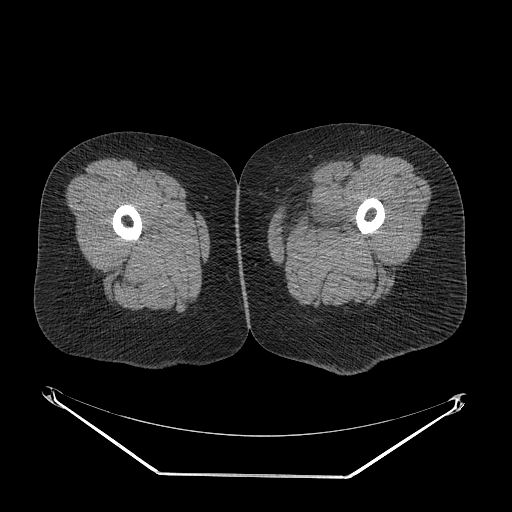
CT of an extremity soft-tissue mass (from a PET/CT study), one axial slice. Position 12 of 267 along the scan axis. Reconstruction kernel STANDARD. Soft-tissue window (W 400 / L 40 HU). 3.75 mm slice thickness. 512 × 512 image matrix. Female patient. From the clinical record (not read from this slice): histological type: myxofibrosarcoma; grade: intermediate; site of the primary tumour: left thigh.
Outlined on this slice (expert contour drawn on MRI and transferred to this co-registered scan by the dataset authors):
- gross tumour volume including surrounding oedema: bounding box <279,201,353,241> (left, top, right, bottom; pixels)